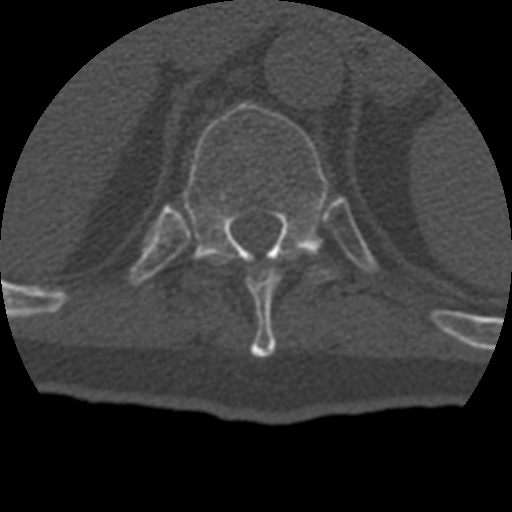
CT including the spine, one axial slice. Position 205 of 399 along the scan axis. Reconstruction kernel STANDARD. Bone window (W 1800 / L 400 HU). 1.25 mm slice thickness. 512 × 512 image matrix, field of view 160 × 160 mm. Patient age 69 years. From the clinical record (not read from this slice): primary cancer: prostate.
Annotated regions visible in this slice (semi-automatically segmented with operator editing):
- T10 vertebra: bounding box [x1, y1, x2, y2] px = [248, 271, 280, 357]
- T11 vertebra: [183, 103, 335, 281]